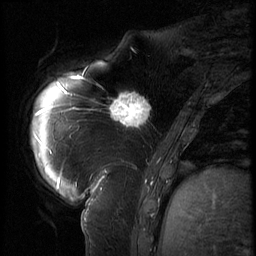
Breast MRI (dynamic contrast-enhanced), one sagittal slice. Slice 18 of 62 in the series (ordered by position). 3 images stored at this slice position (order not interpretable as contrast timing). 1.5 T. TE 4.2 ms, TR 9 ms. 2.5 mm slice thickness. 256 × 256 image matrix. Patient: female, 57 years. From the clinical record (not read from this slice): setting: breast cancer imaged before/during neoadjuvant chemotherapy; receptor status: triple-negative.
Structures marked on this image (semi-automatically segmented with operator editing):
- analysis volume of interest (the breast-tissue region the enhancement analysis was run in; not a lesion): box from (x=105, y=84) to (x=158, y=135) px
- tumour enhancement mask (voxels above the 140 % enhancement threshold inside the analysis volume of interest): (x=110, y=92)–(x=152, y=127)